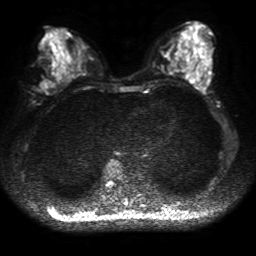
Breast MRI, one axial slice. Position 23 of 50 along the scan axis. Diffusion-weighted series; image 2 of 4 stored at this slice position (different b-values; order by instance number). 1.5 T. 4 mm slice thickness. 256 × 256 image matrix, field of view 320 × 320 mm. Female patient.
Annotated regions visible in this slice (outlined manually by an expert reader):
- tumour on diffusion-weighted imaging: box from (x=40, y=80) to (x=55, y=94) px